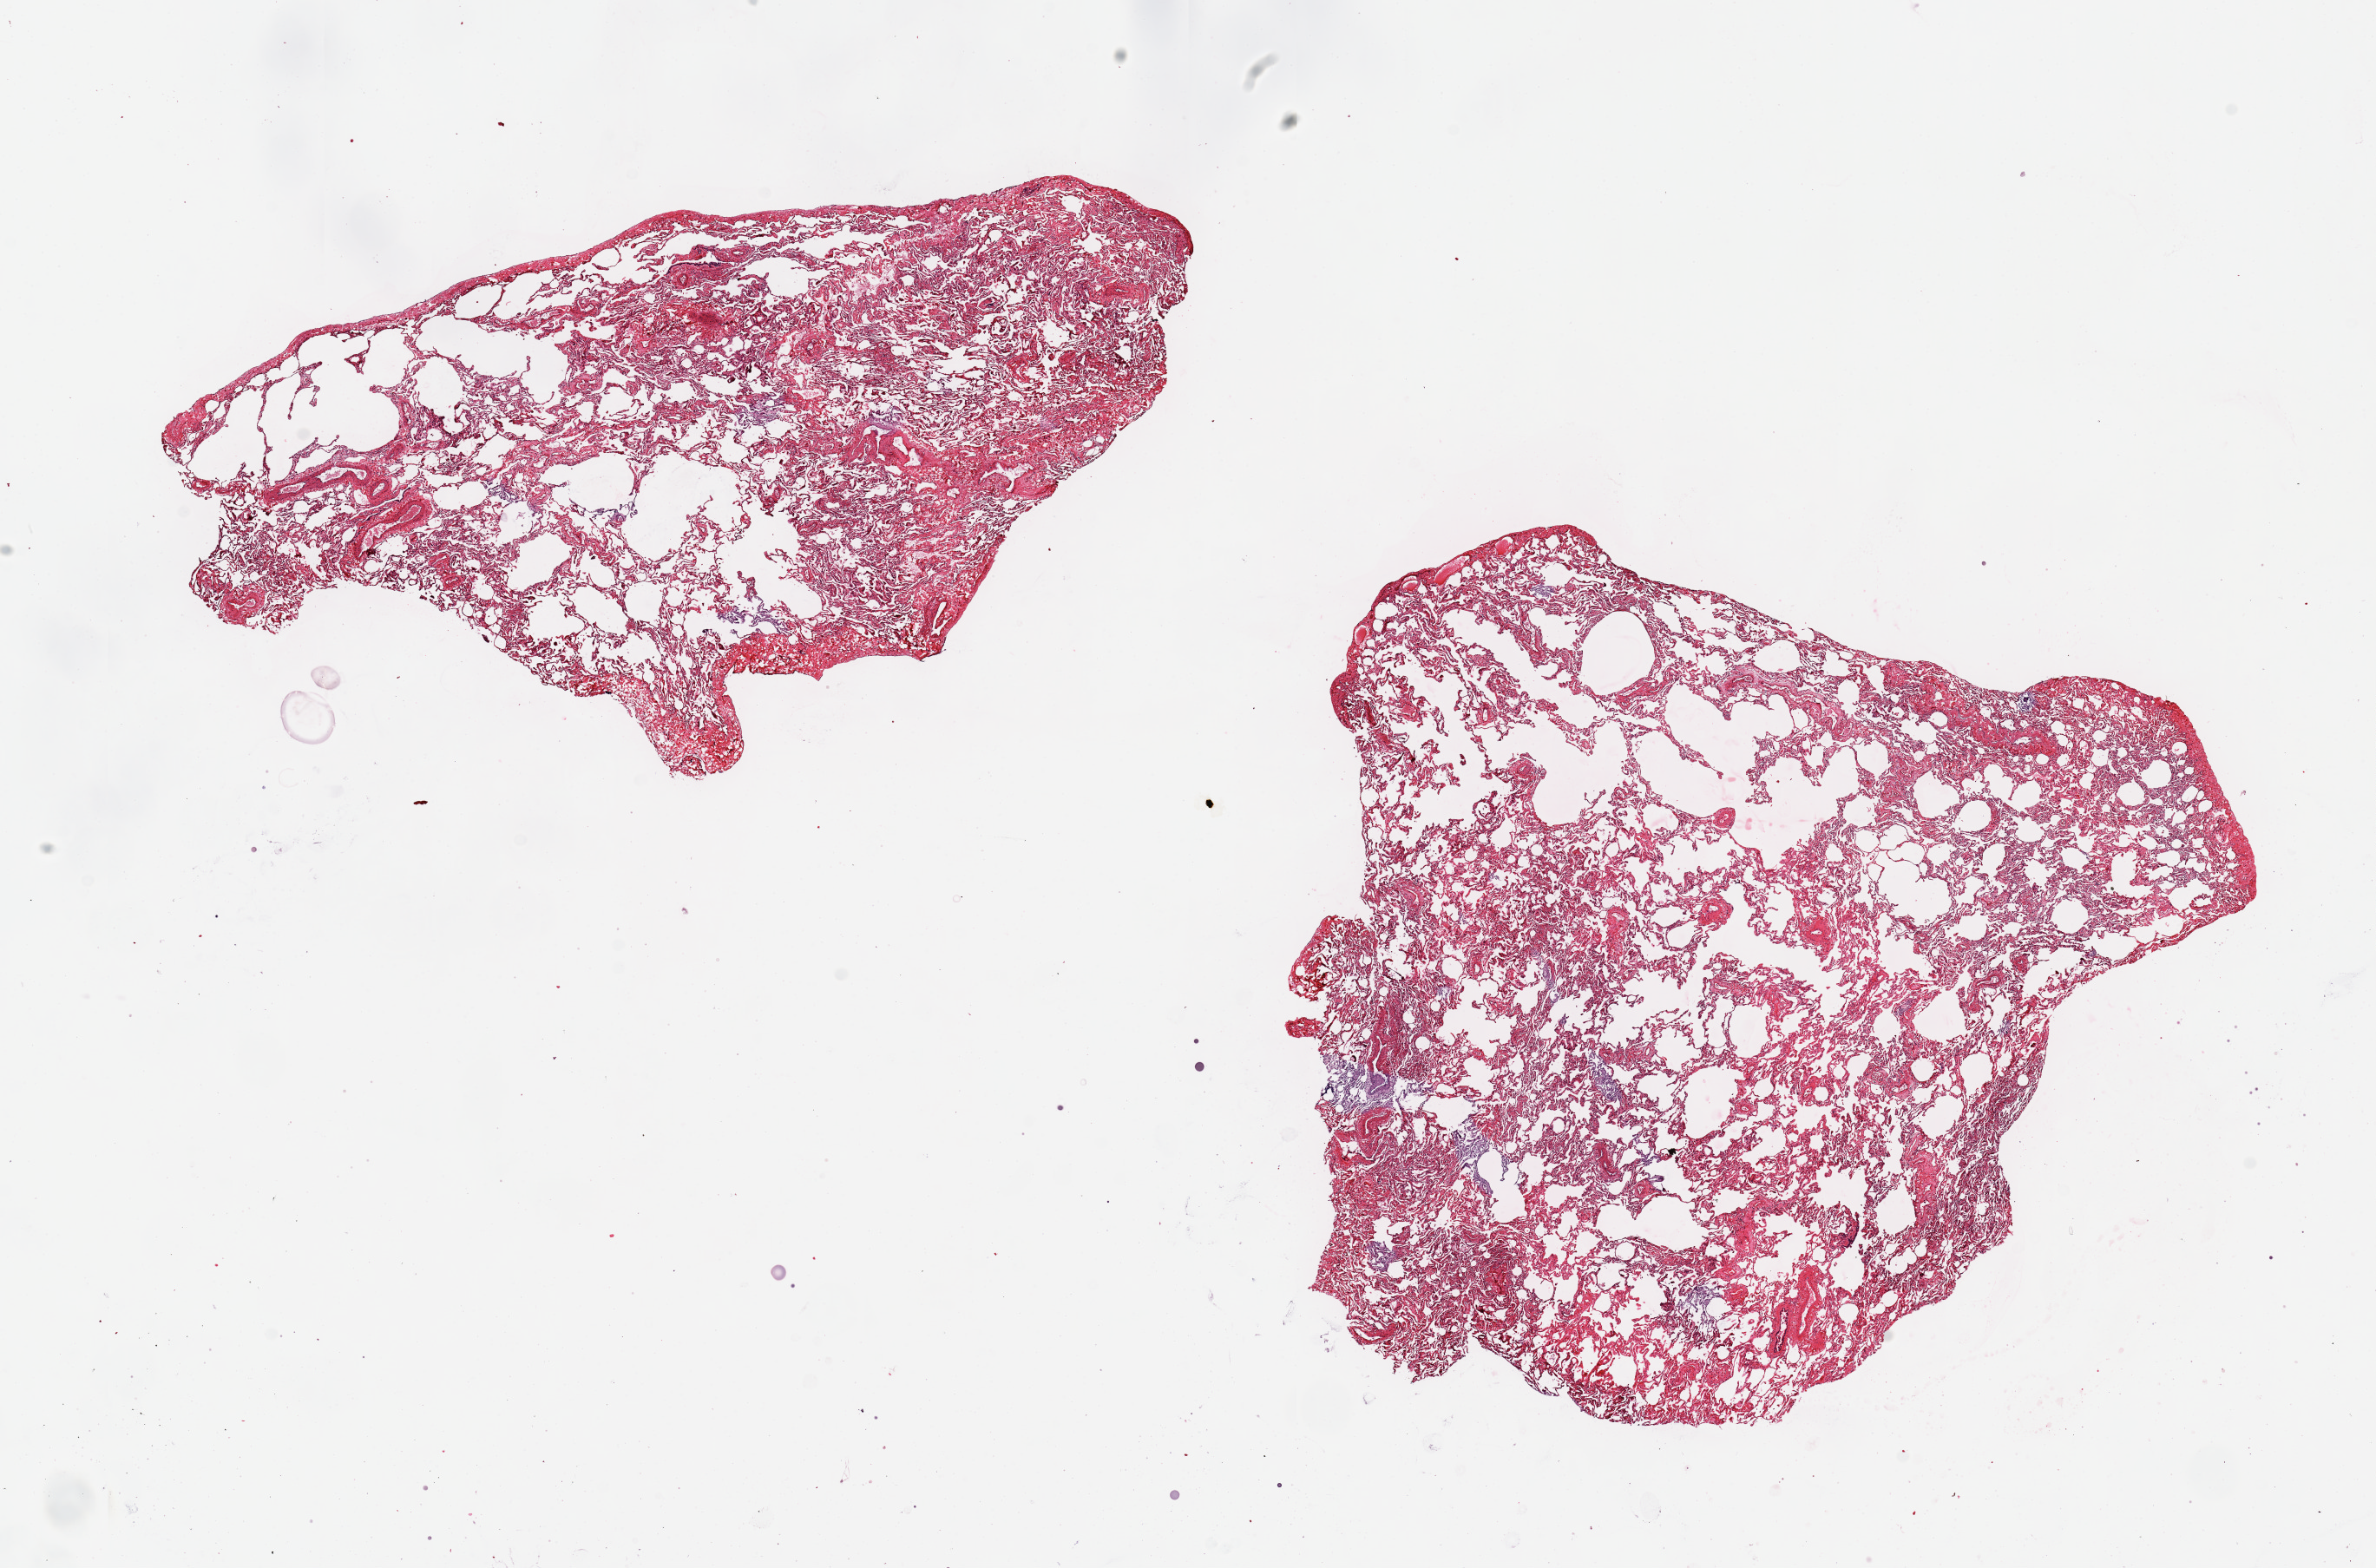
Digitized haematoxylin and eosin-stained section, shown as a low-resolution overview of the whole scanned area (about 21.7 x 14.3 mm, from a 20x scan). PAXgene-fixed paraffin-embedded (PFPE) section. Target tissue: lung. Tissue donor sample. Donor sex: male.
Reviewer comment on this tissue sample: 2 pieces ~9x2mm, minimal congestion.